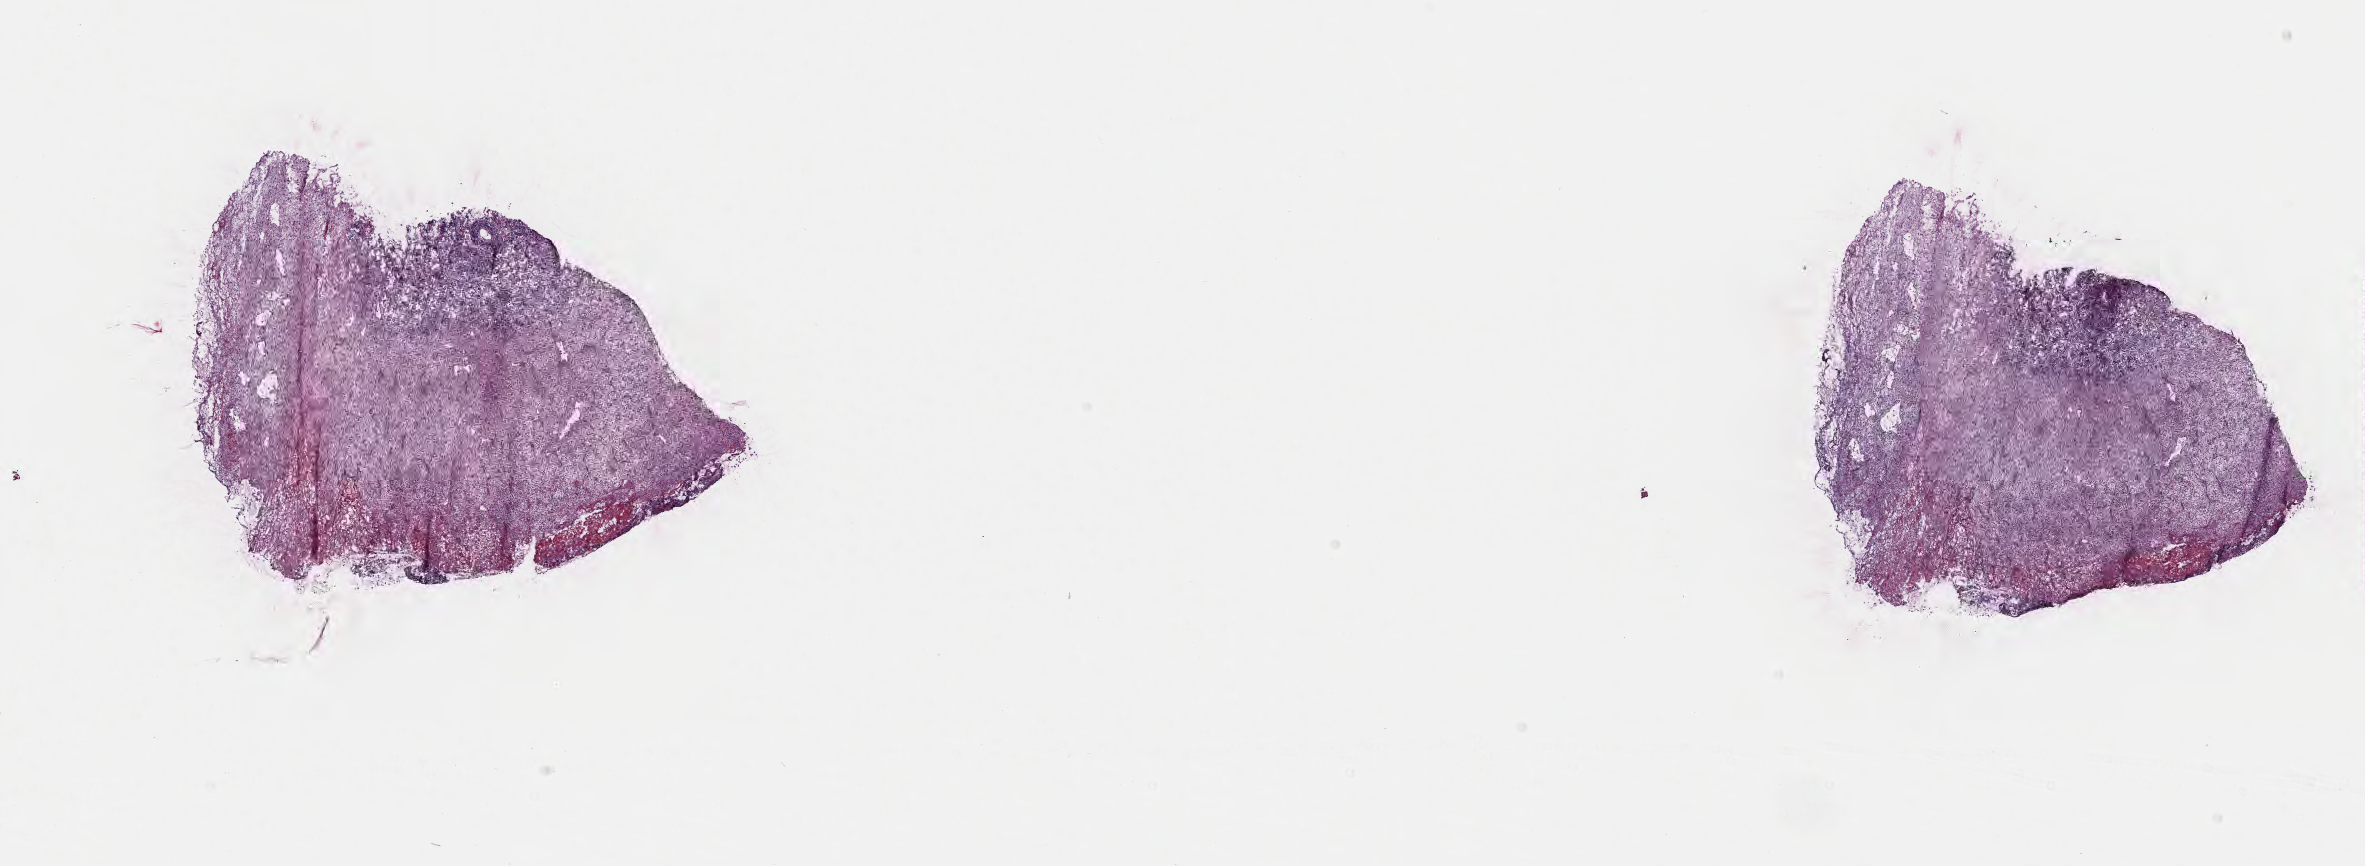
Whole-slide image, hematoxylin and eosin (H&E) stain, a low-resolution overview of the entire scanned area, about 19.1 x 7.0 mm. Frozen section (tissue freezing medium). Specimen: primary tumor. Anatomic site: cranium. Patient: male, age at initial diagnosis 2 years. Slide review estimates, as recorded: tumor cells 20%, tumor nuclei 75%, stromal cells 65%, necrosis 15%, normal cells 0%. Infiltration values recorded for this section: lymphocyte infiltration 20%, monocyte infiltration 35%, neutrophil infiltration 15%.
Histologic diagnosis: Burkitt lymphoma, NOS. Section: bottom of the tissue portion. Ann Arbor stage (patient): Stage I.